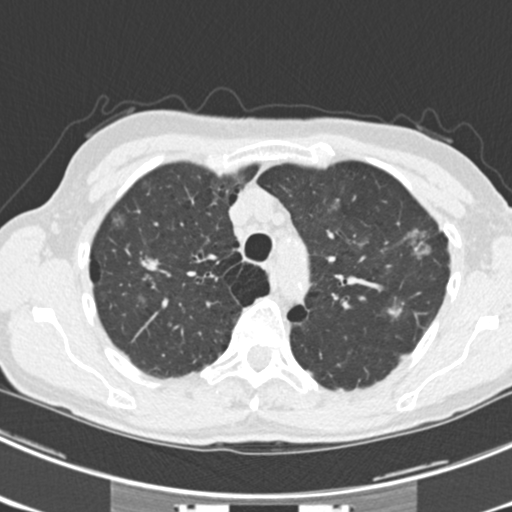
Low-dose screening chest CT, one axial slice; position 171 of 225 along the scan axis; lung window (W 1500 / L -600 HU); 512 × 512 image matrix.
Outlined on this slice (outlined manually by an expert reader):
- lesion 3 (tumor, upper lobe of right lung): bounding box <140,256,160,271> (left, top, right, bottom; pixels)